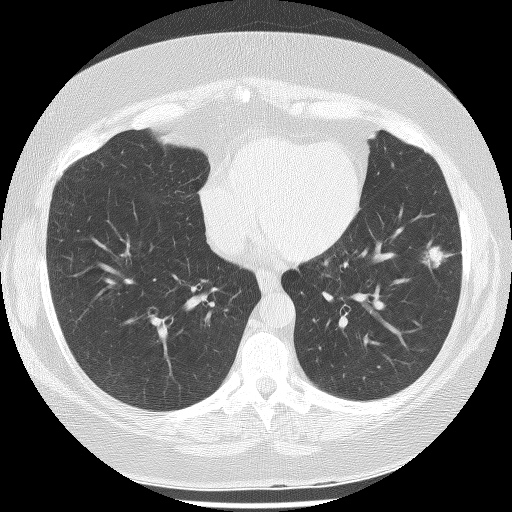
Low-dose screening chest CT, one axial slice. Position 100 of 233 along the scan axis. Reconstruction kernel BONE. 120 kVp. Lung window (W 1500 / L -600 HU). 512 × 512 image matrix, field of view 340 × 340 mm.
Structures marked on this image (outlined manually by an expert reader):
- lesion 1 (tumor, lower lobe of left lung): box from (x=423, y=241) to (x=454, y=271) px